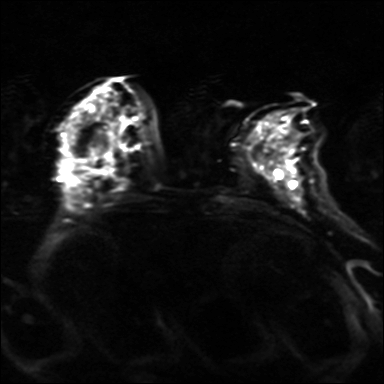
Breast MRI, one axial slice. Slice 15 of 36 in the series (ordered by position). Diffusion-weighted series; image 2 of 4 stored at this slice position (different b-values; order by instance number). 3 T. 4 mm slice thickness. 384 × 384 image matrix. Female patient.
Outlined on this slice (expert manual segmentation):
- tumour on diffusion-weighted imaging: bounding box (x1, y1, x2, y2) in pixels: (288, 146, 296, 171)